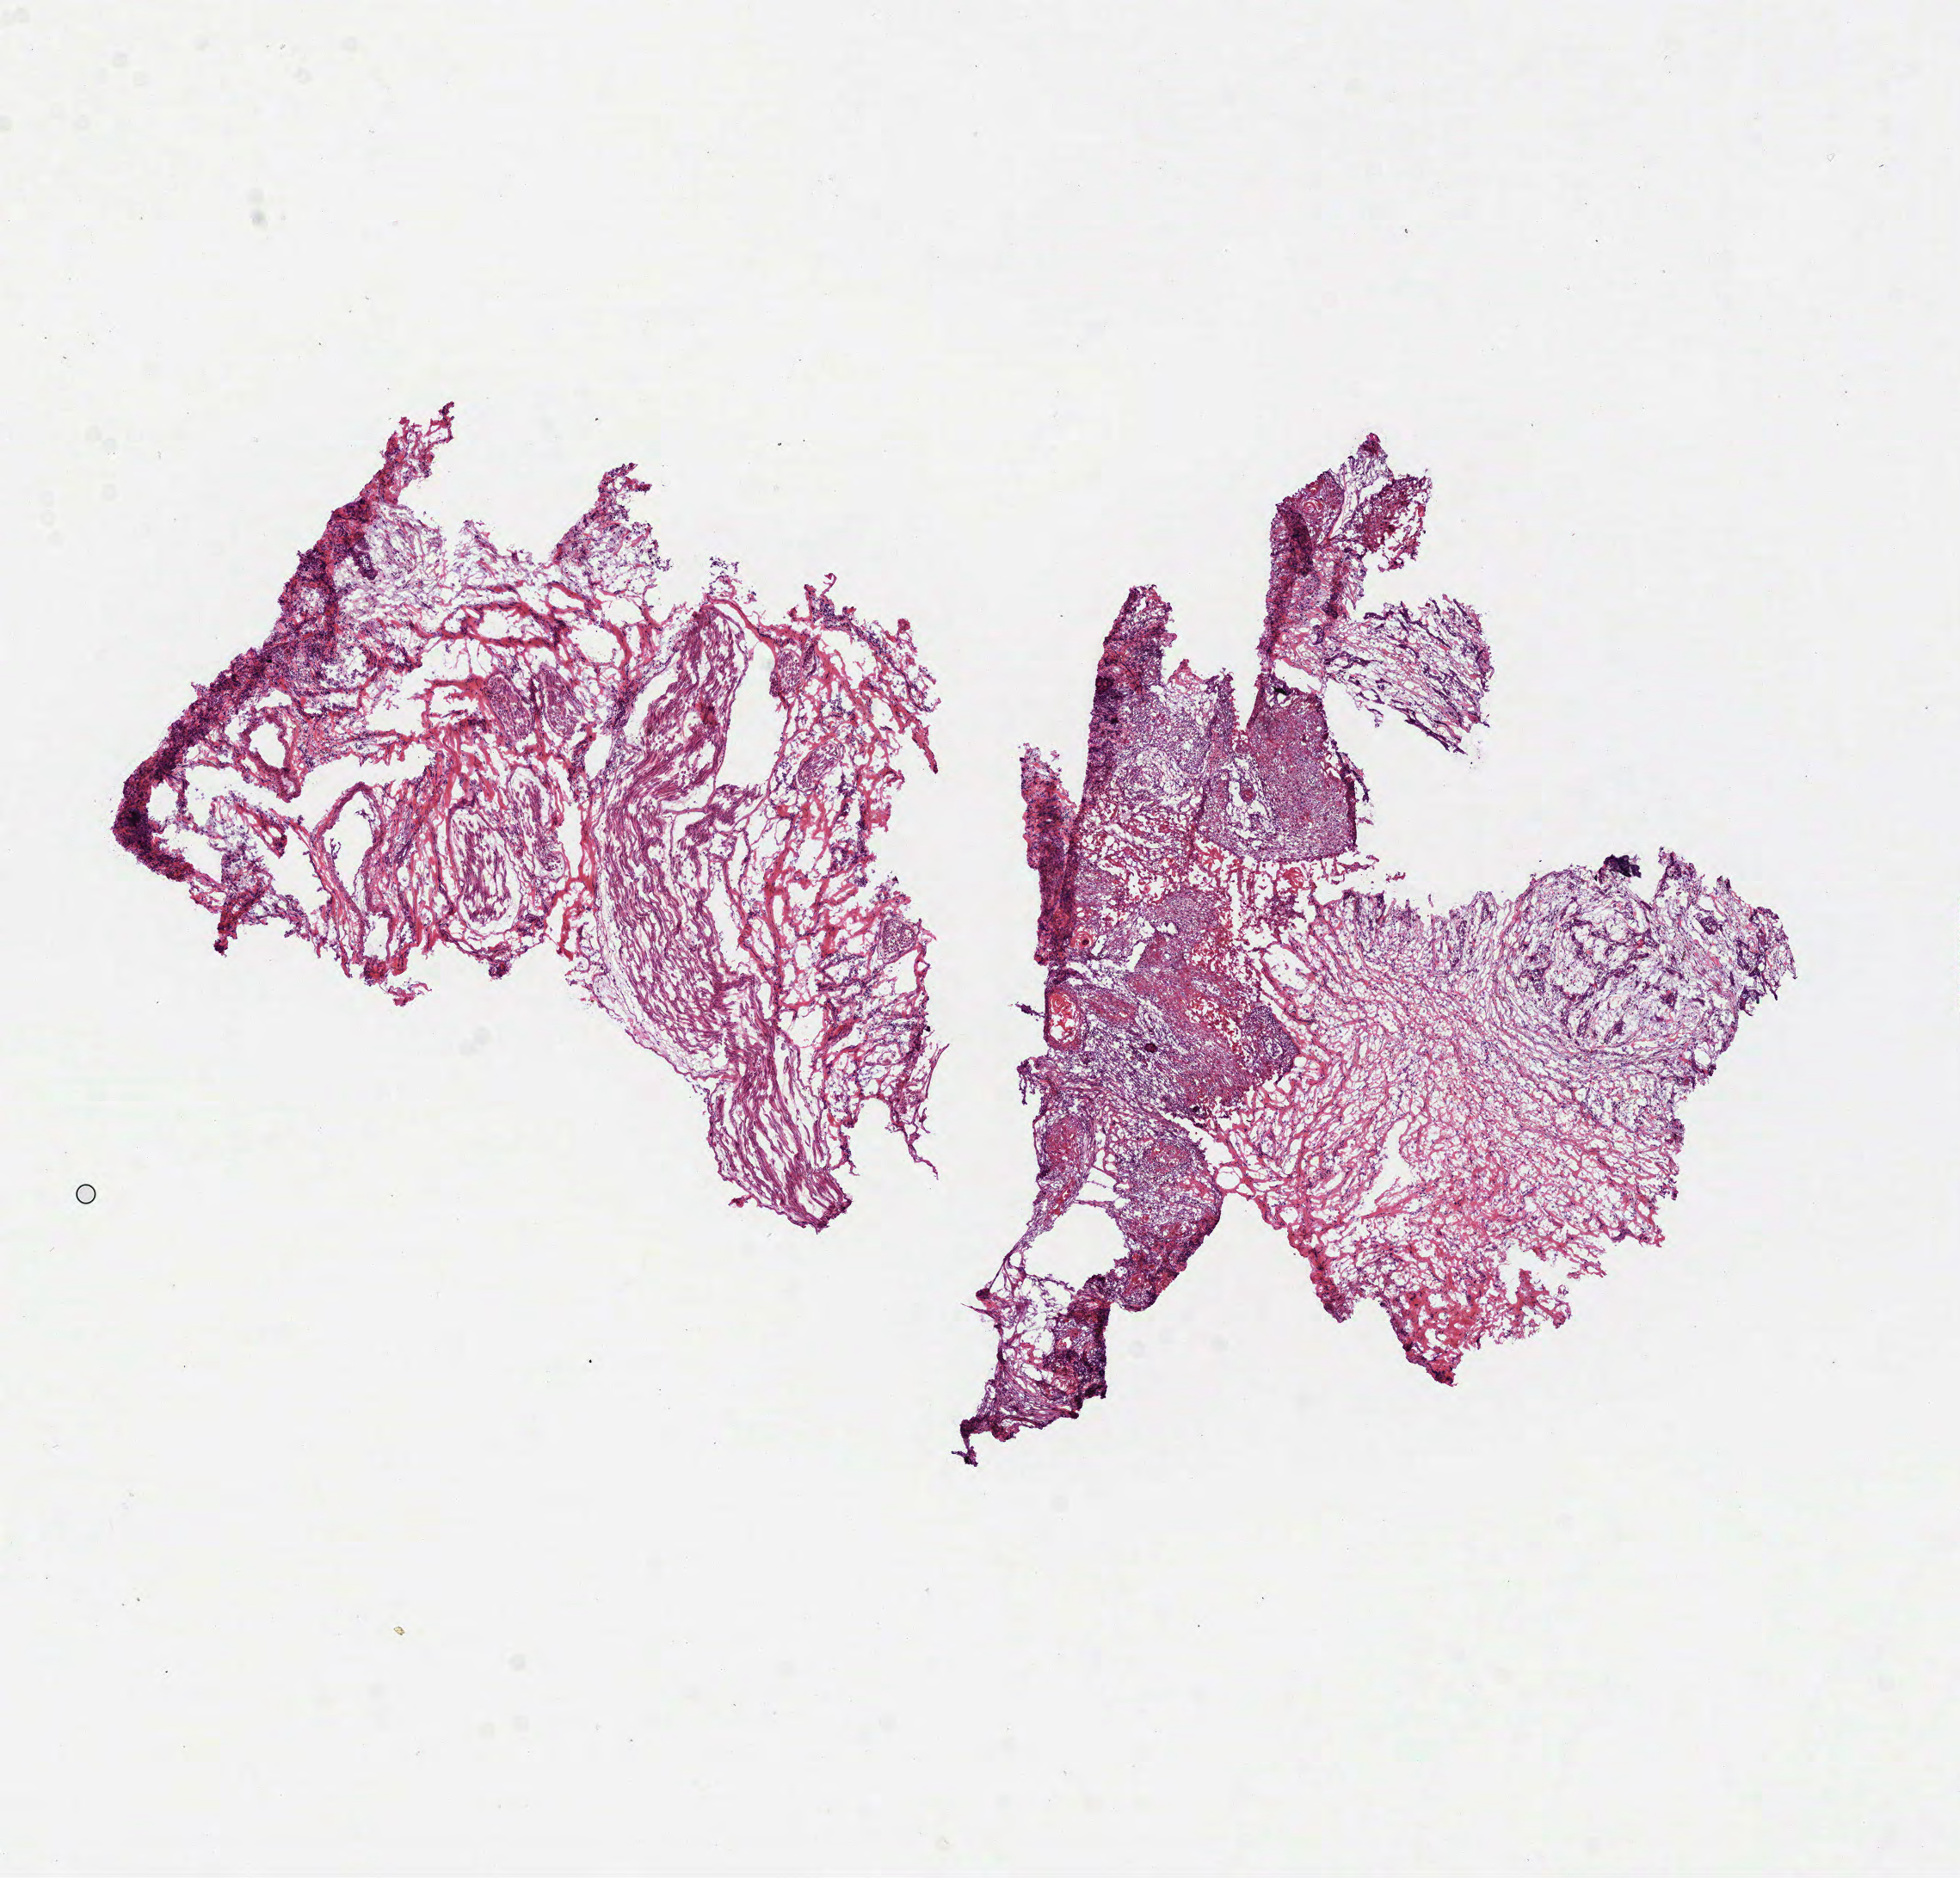
H&E-stained whole-slide image — whole scanned area (about 9.2 x 8.8 mm, acquisition: 40x scan) shown as a low-resolution overview; frozen section from the bottom of the tissue portion; head and neck, primary tumour sample. Female patient; age at initial diagnosis 66 years. Histologic grade: G2 (moderately differentiated). Slide review estimates, as recorded: tumour cells 20%, tumour nuclei 30%, normal cells 70%, stromal cells 0%, necrosis 10%. Infiltration values recorded for this section: lymphocyte infiltration 10%, monocyte infiltration 0%, neutrophil infiltration 2%.
• pathologic diagnosis: Squamous cell carcinoma, NOS (tongue, NOS)
• AJCC pathologic stage: IVA (7th edition)